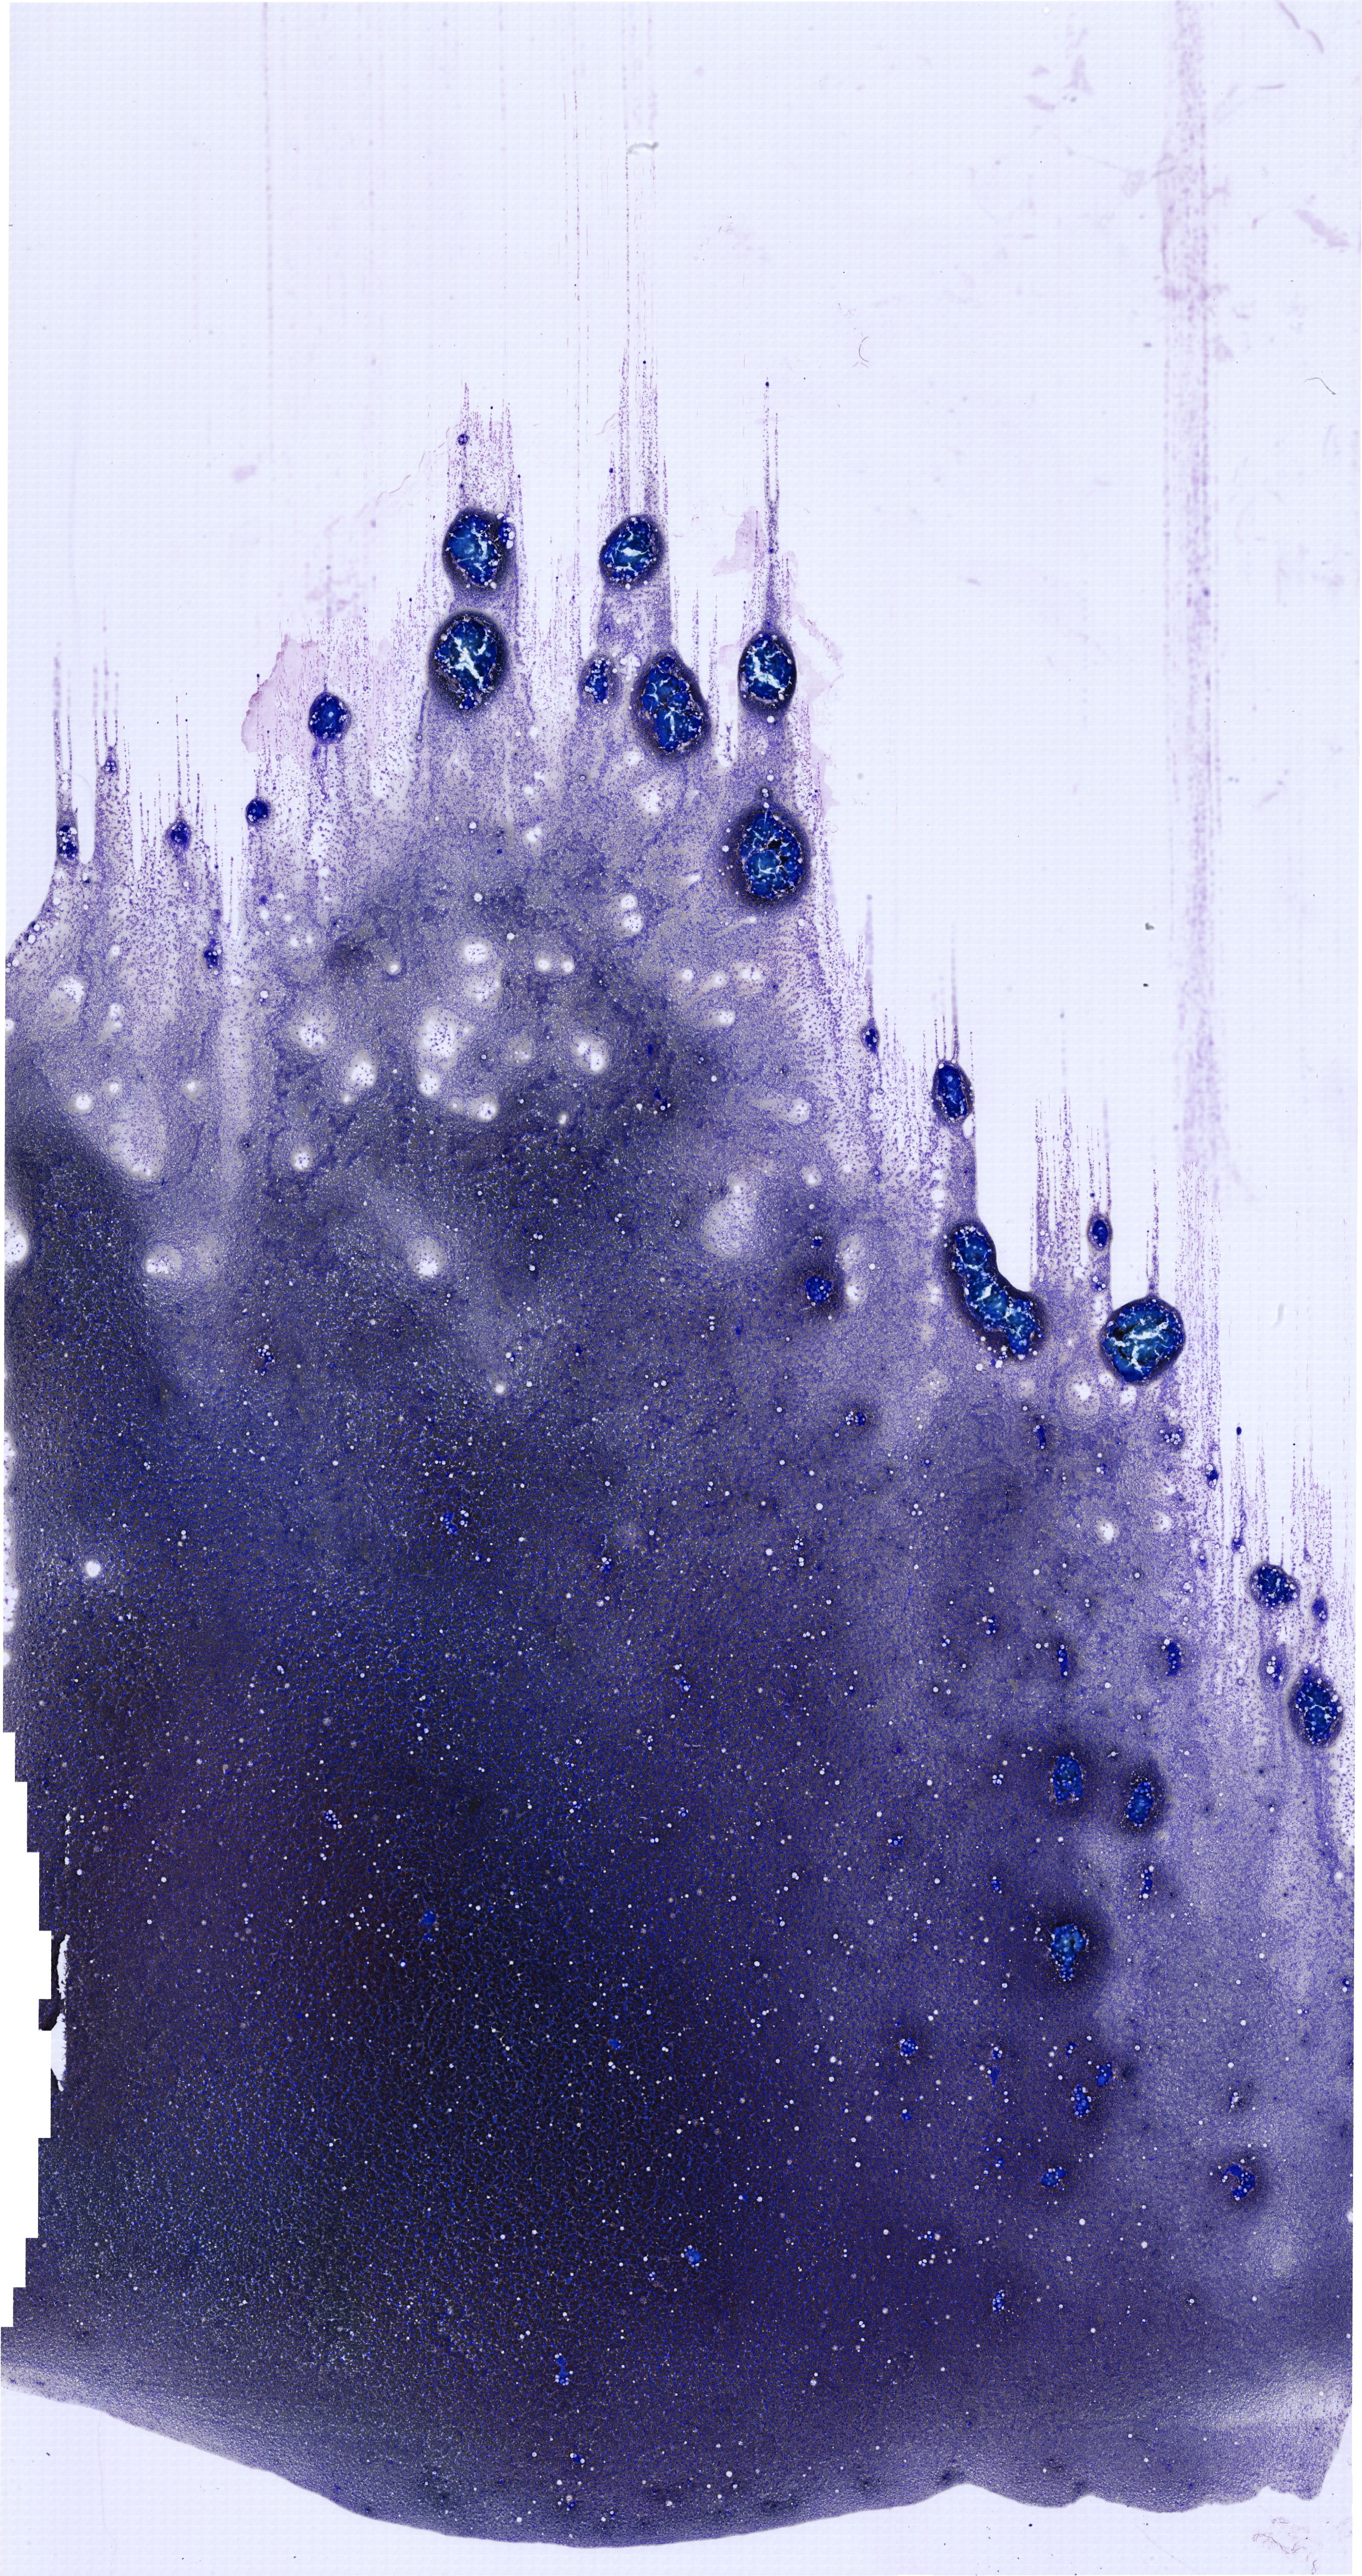
May-Grünwald–Giemsa-stained marrow aspirate smear (whole slide), low-resolution overview of the scanned area, about 21.5 x 40.6 mm. Male patient.
- diagnosis: T Acute Lymphoblastic Leukemia